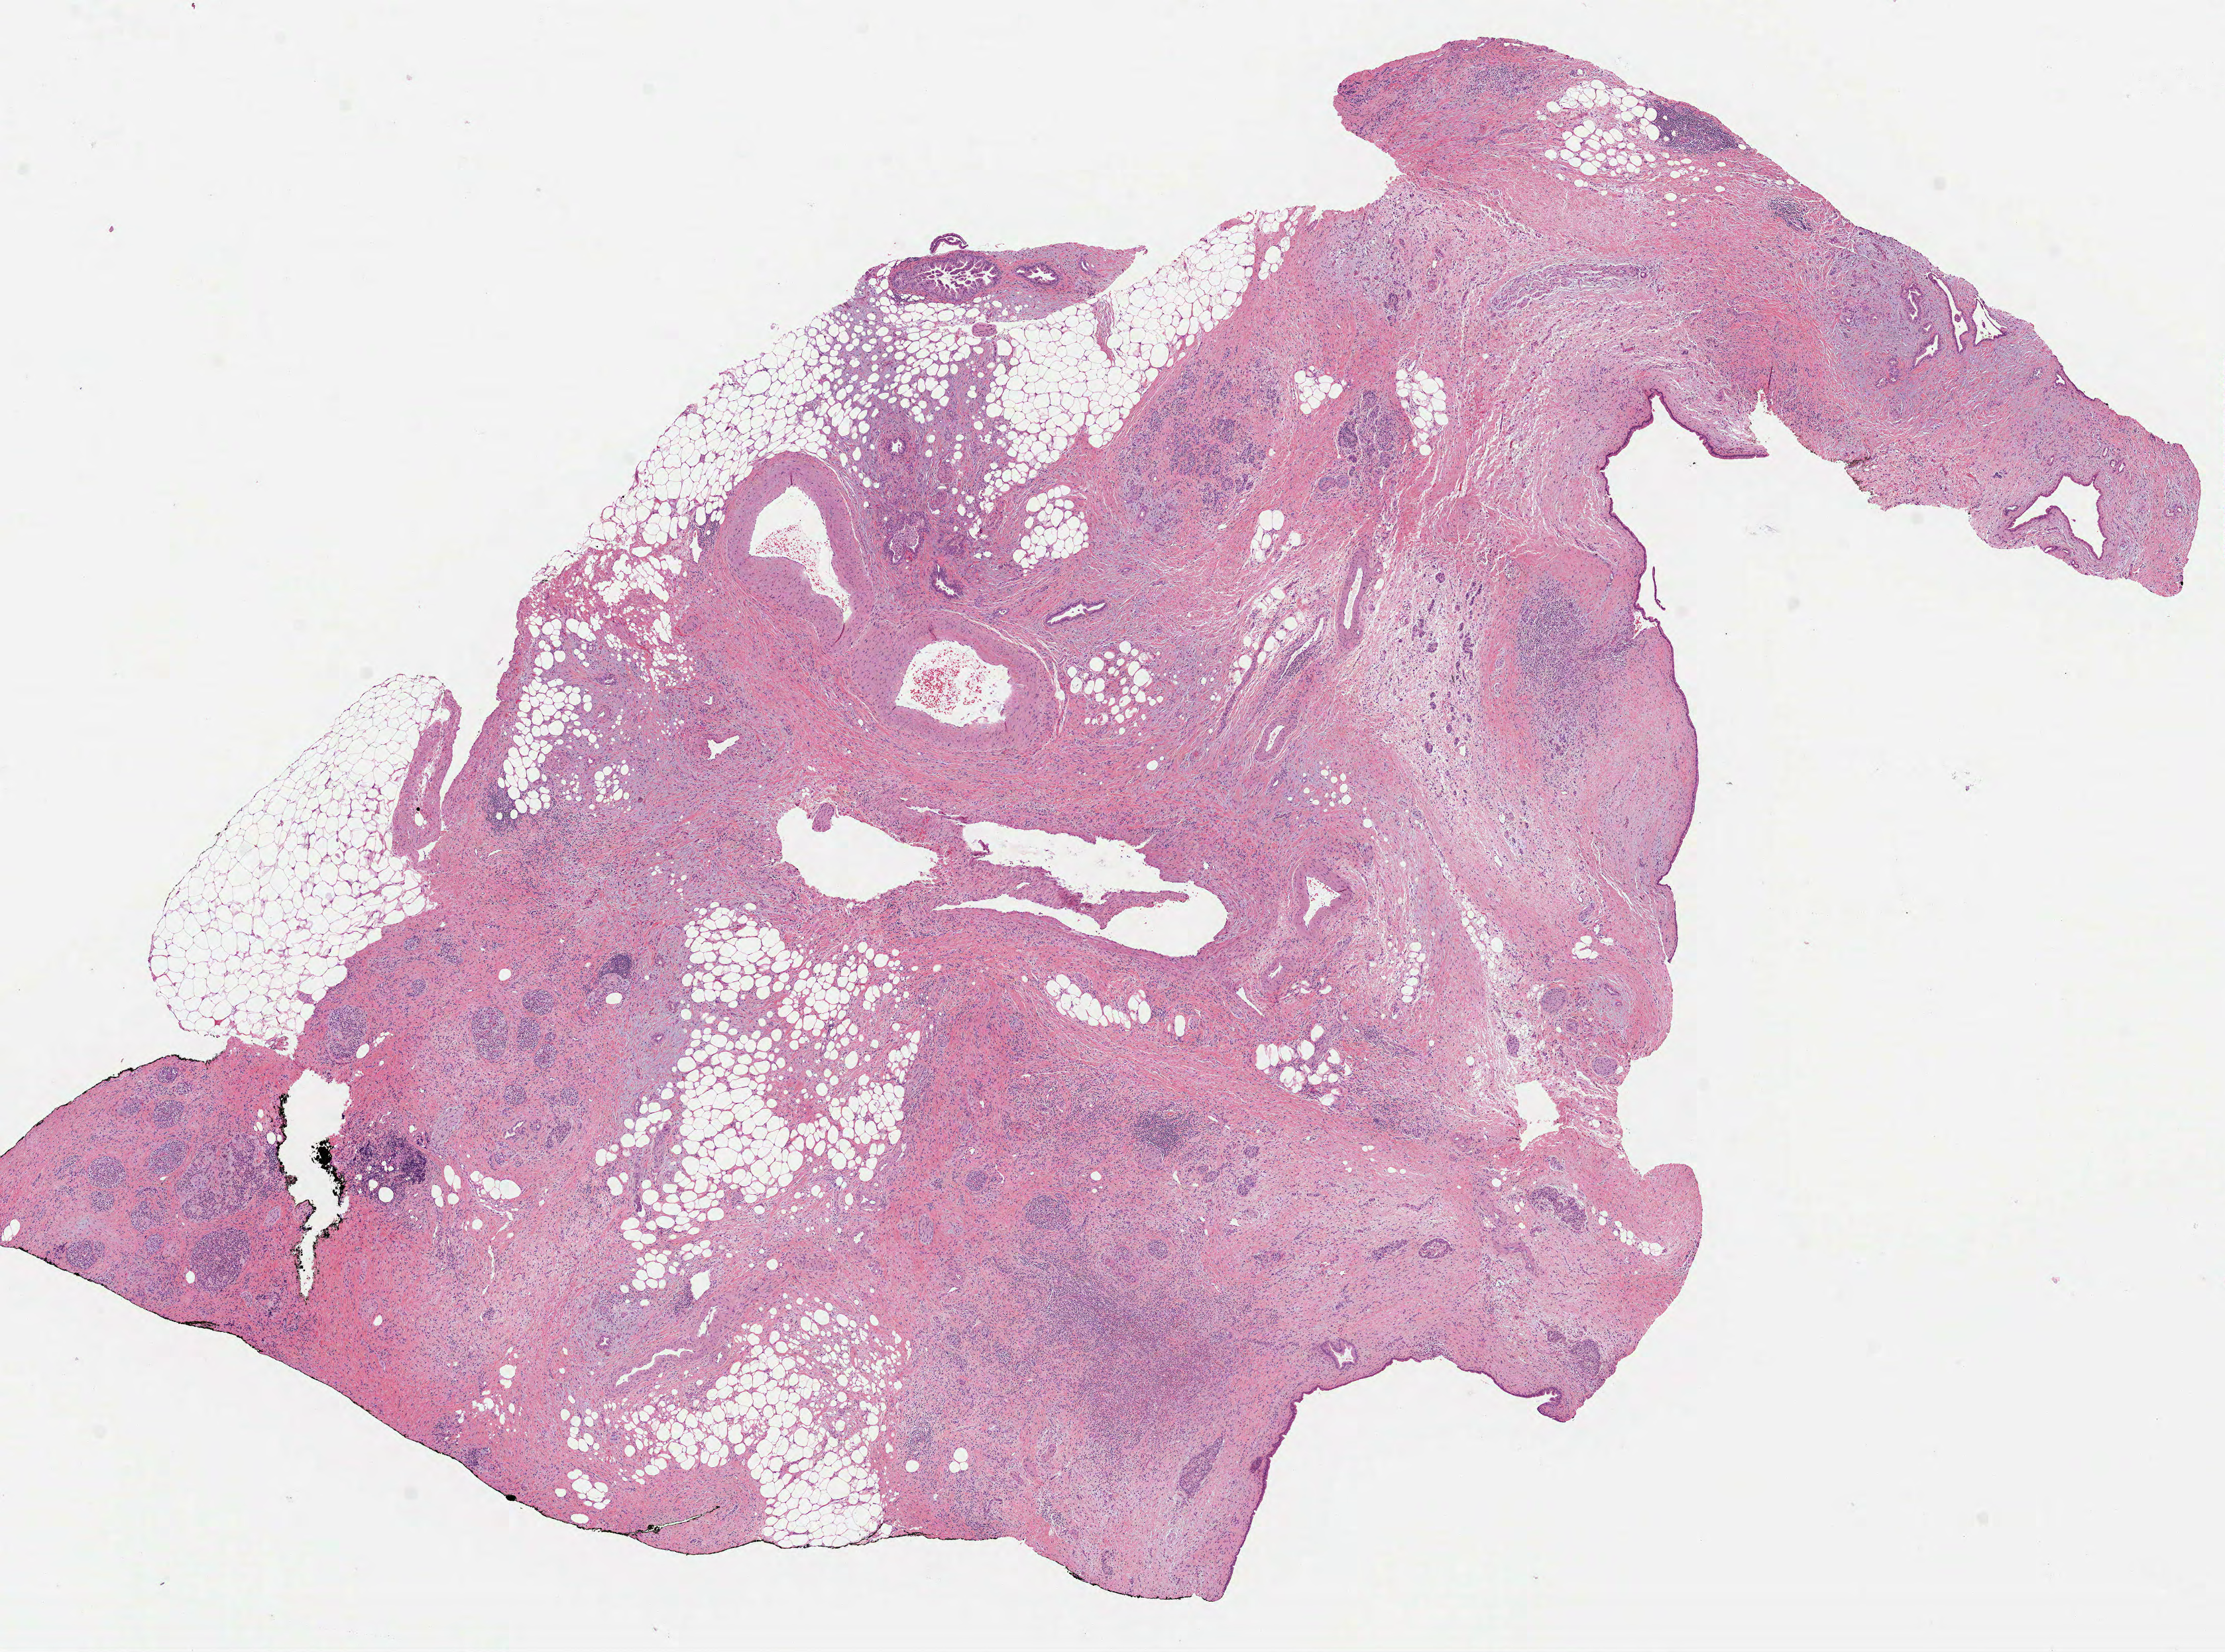
Whole-slide histology image, H&E-stained — whole scanned area (about 13.5 x 10.1 mm, from a 40x scan) shown as a low-resolution overview. Formalin-fixed paraffin-embedded (FFPE) diagnostic section. Sample: primary tumour, pancreas. Male, age 71 years at initial diagnosis.
Histologic diagnosis: Infiltrating duct carcinoma, NOS (head of pancreas).